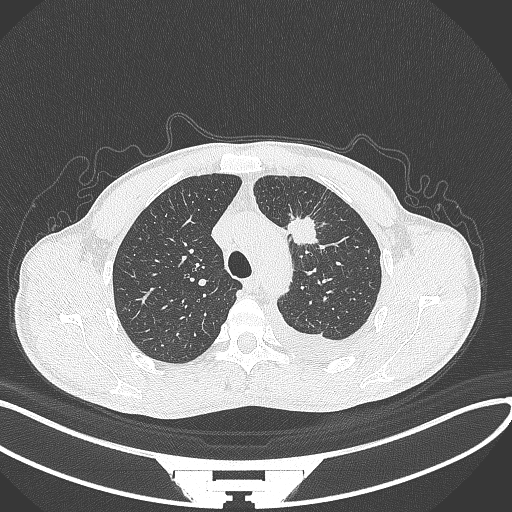
Chest CT, one axial slice; slice 256 of 371 in the series (ordered by position); 120 kVp; lung window (W 1500 / L -600 HU); 1 mm slice thickness; 512 × 512 image matrix, field of view 400 × 400 mm. Patient: male, 49 years. From the clinical record (not read from this slice): clinical TNM (as recorded): T1c N1 M1.
Structures marked on this image (rectangle marked by the reading radiologist):
- lung tumour (recorded histology: adenocarcinoma): bounding box <285,214,323,250> (left, top, right, bottom; pixels)